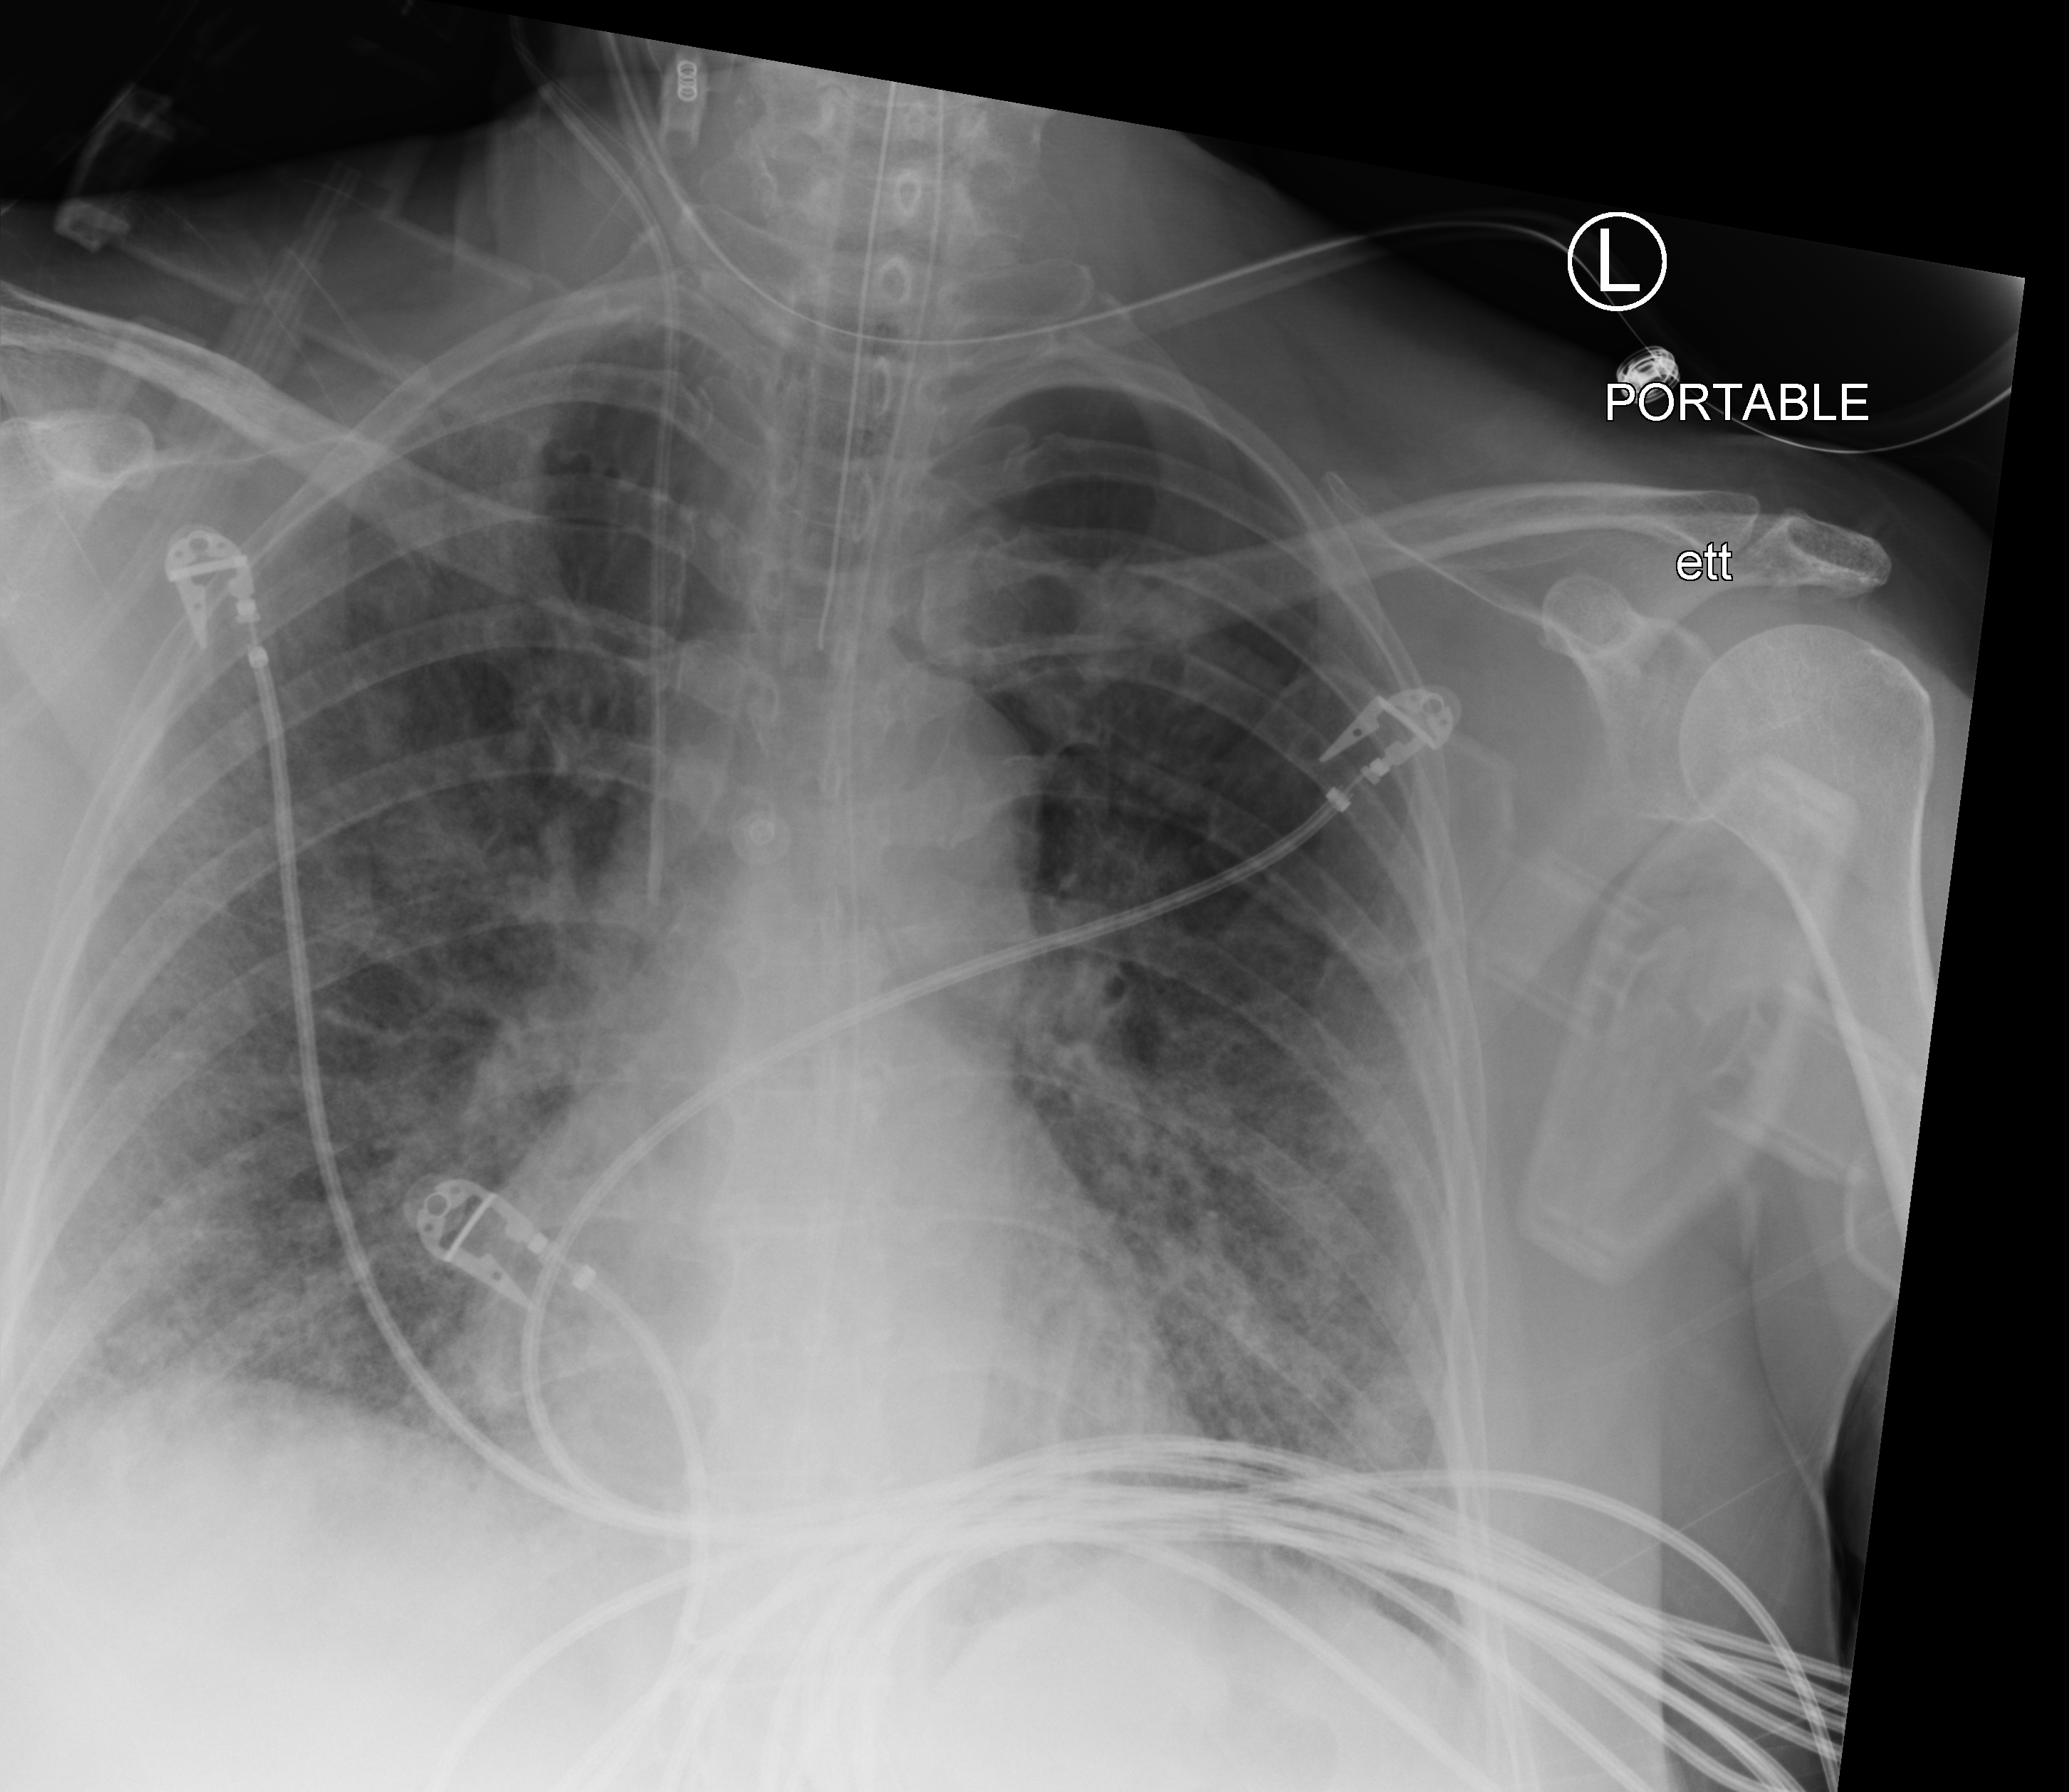
Chest X-ray (portable), anteroposterior (AP) projection. Patient hospitalised with COVID-19; female, aged 60–74 years.
Admission-level facts for this patient (not findings on this image; timing relative to this image not recorded): length of hospital stay: 43 days.